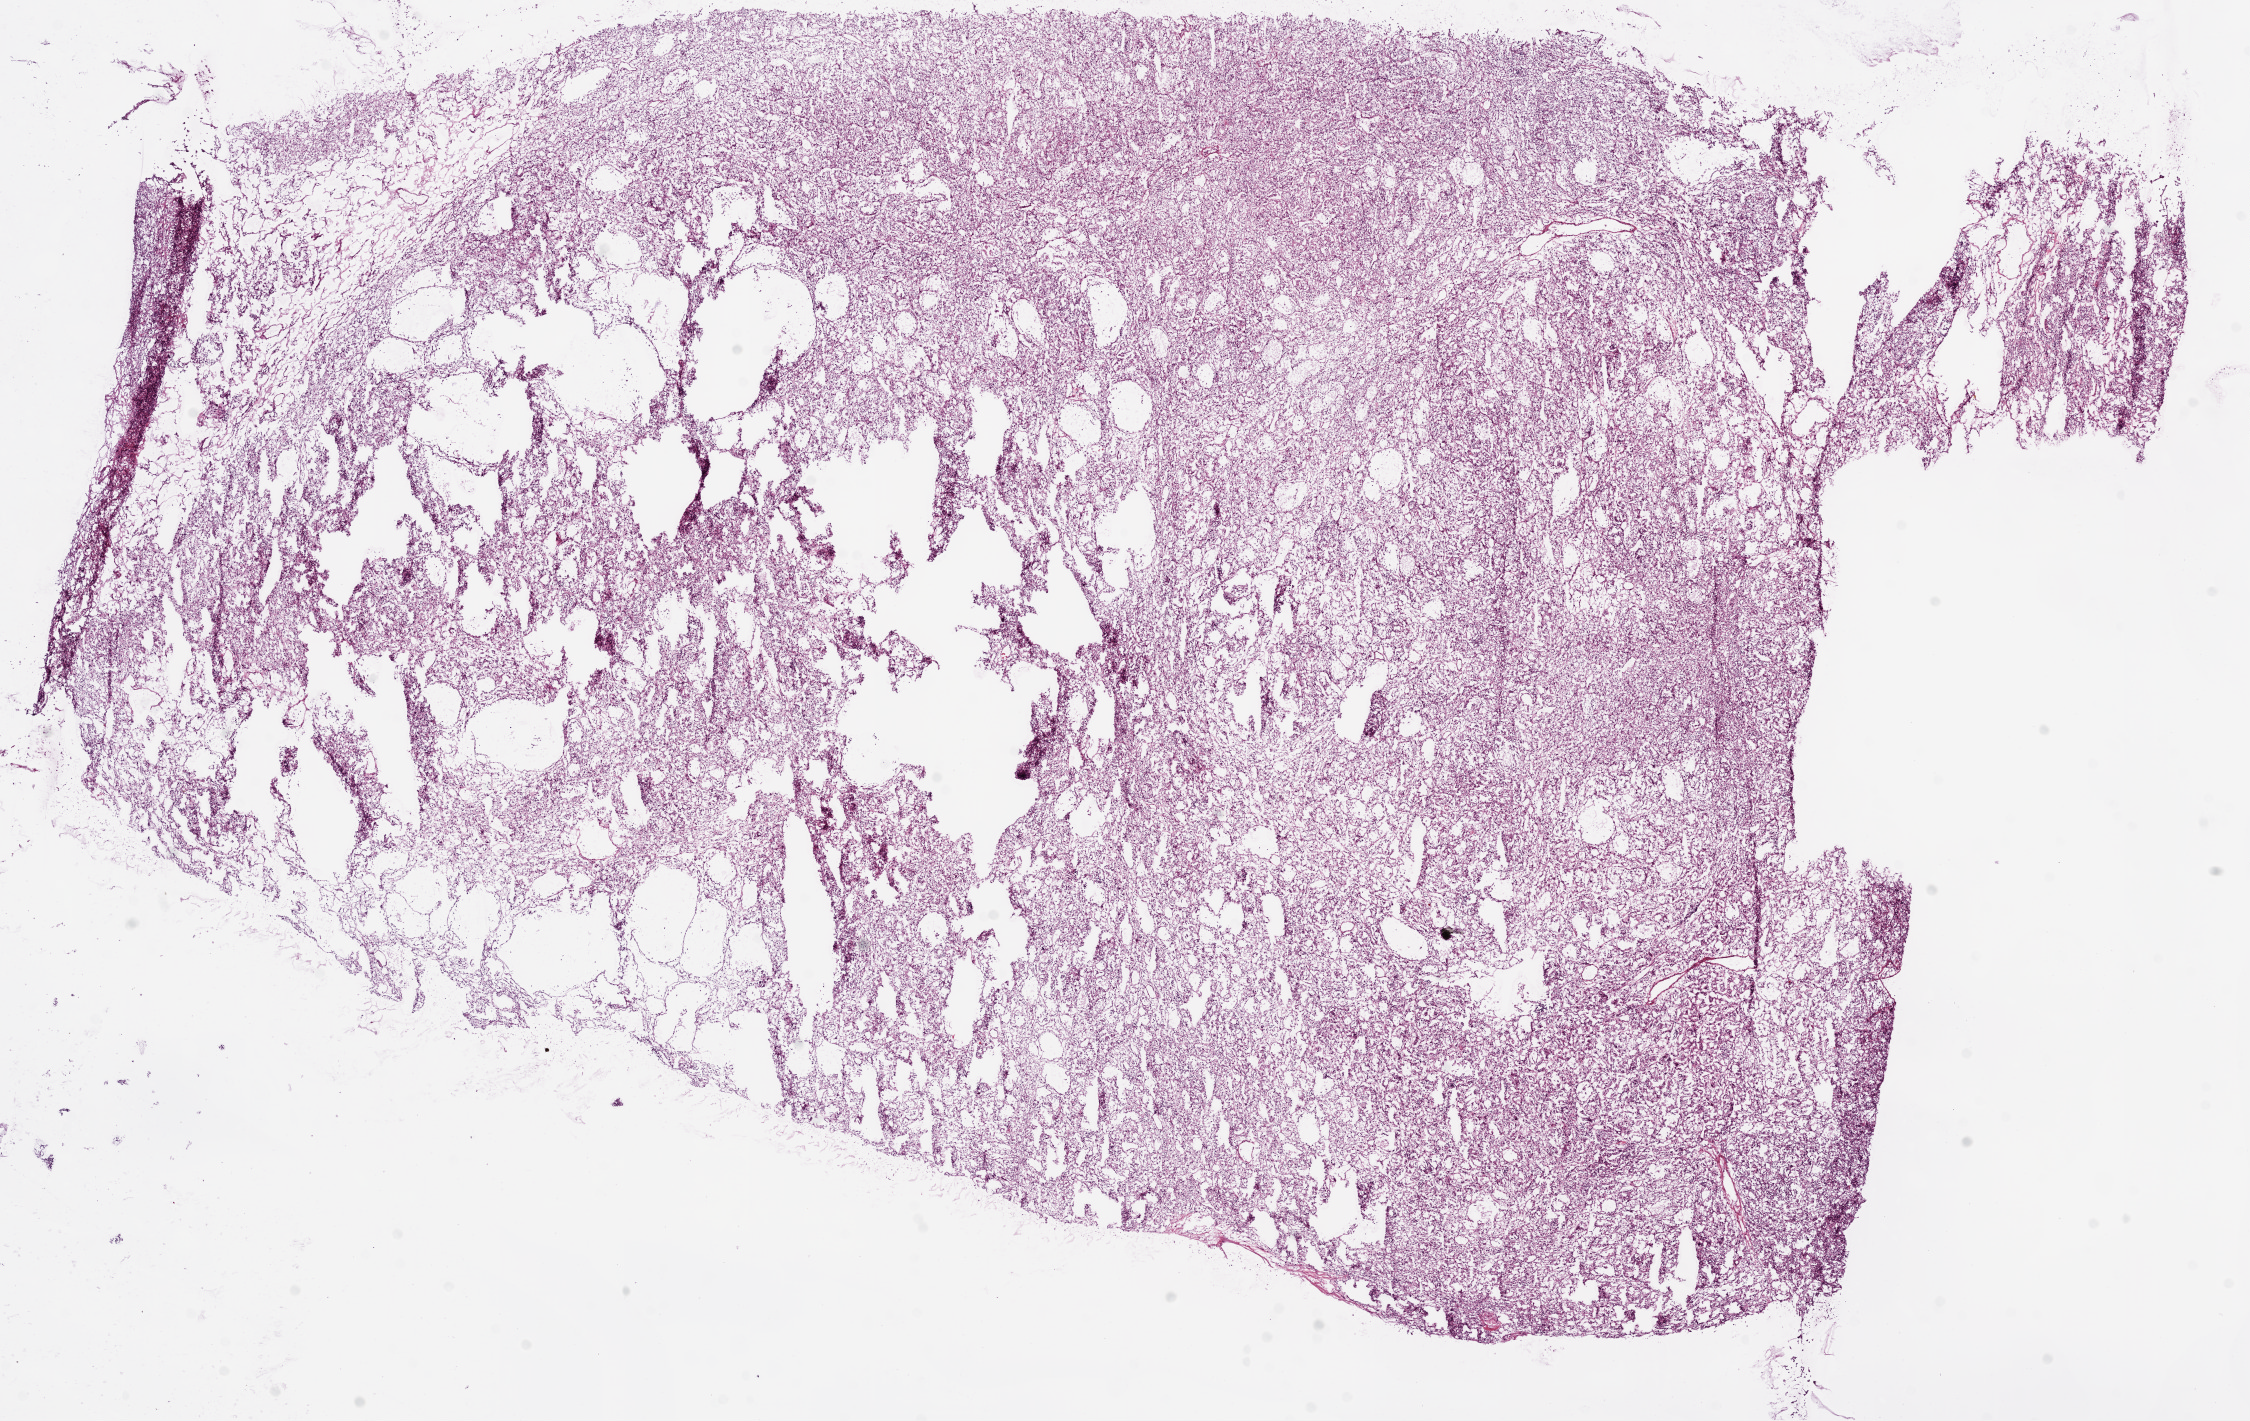
H&E-stained whole-slide image, low-resolution overview of the scanned area, about 18.1 x 11.4 mm (acquisition: 20x scan), frozen section, kidney, primary tumour sample. Female patient; age at initial diagnosis 49 years. Histologic grade: G3 (poorly differentiated). Composition of this section per pathologist review: tumour cells 95%, tumour nuclei 85%, normal cells 0%, stromal cells 5%, necrosis 0%.
AJCC pathologic stage: I. Pathologic diagnosis: Clear cell adenocarcinoma, NOS.